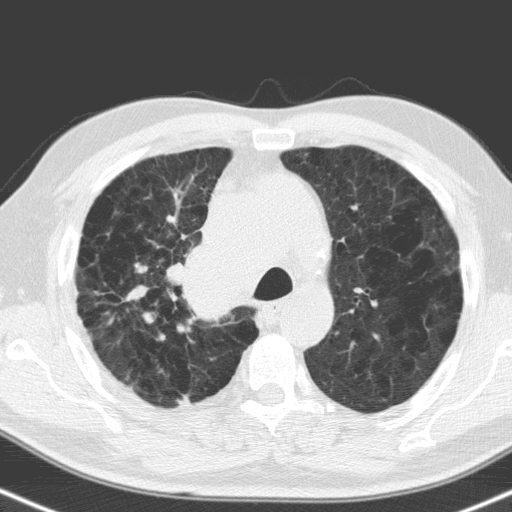
Low-dose screening chest CT, one axial slice; slice 120 of 160 in the series (ordered by position); lung window (W 1500 / L -600 HU); 3.2 mm slice thickness; 512 × 512 image matrix, field of view 324 × 324 mm.
Annotated regions visible in this slice (outlined manually by an expert reader):
- lesion 1 (tumor, hilum of right lung): box from (x=170, y=247) to (x=240, y=320) px